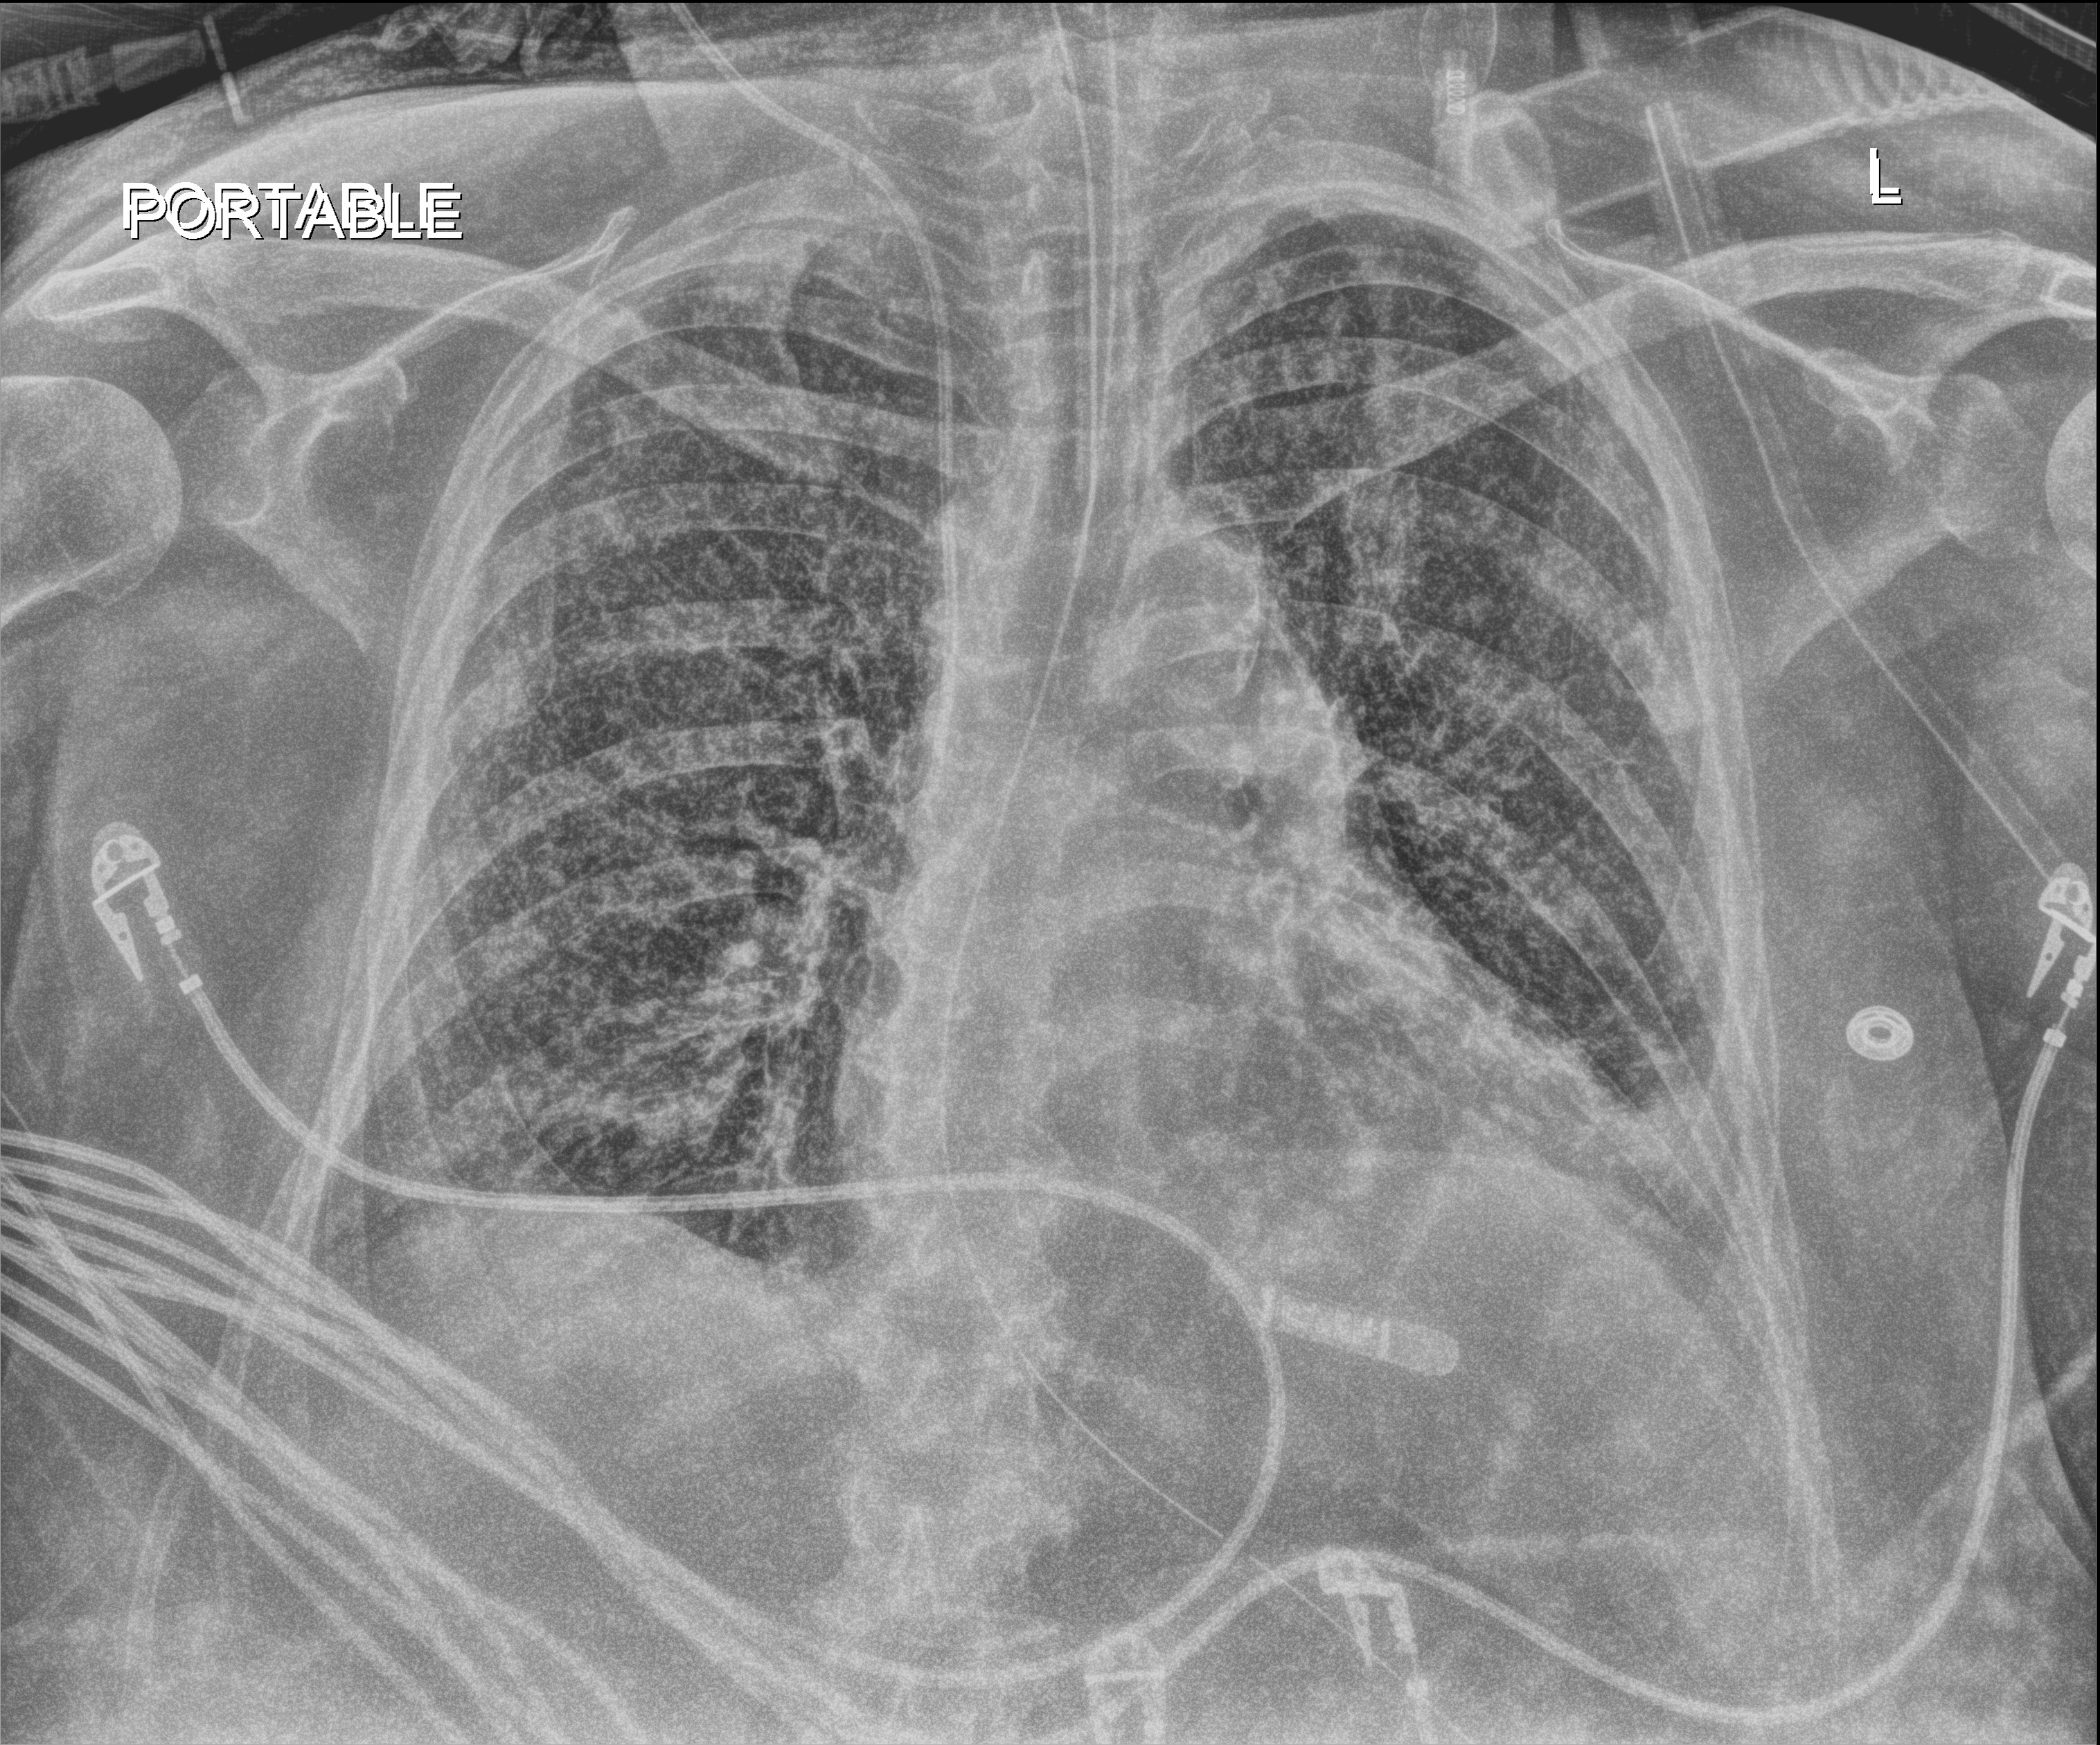
Portable chest radiograph; anteroposterior (AP) projection. Patient hospitalised with COVID-19; female, aged 60–74 years.
Hospital-stay facts (about this admission, not read from this image; timing relative to this image not recorded): admitted to intensive care during this hospital stay: yes.